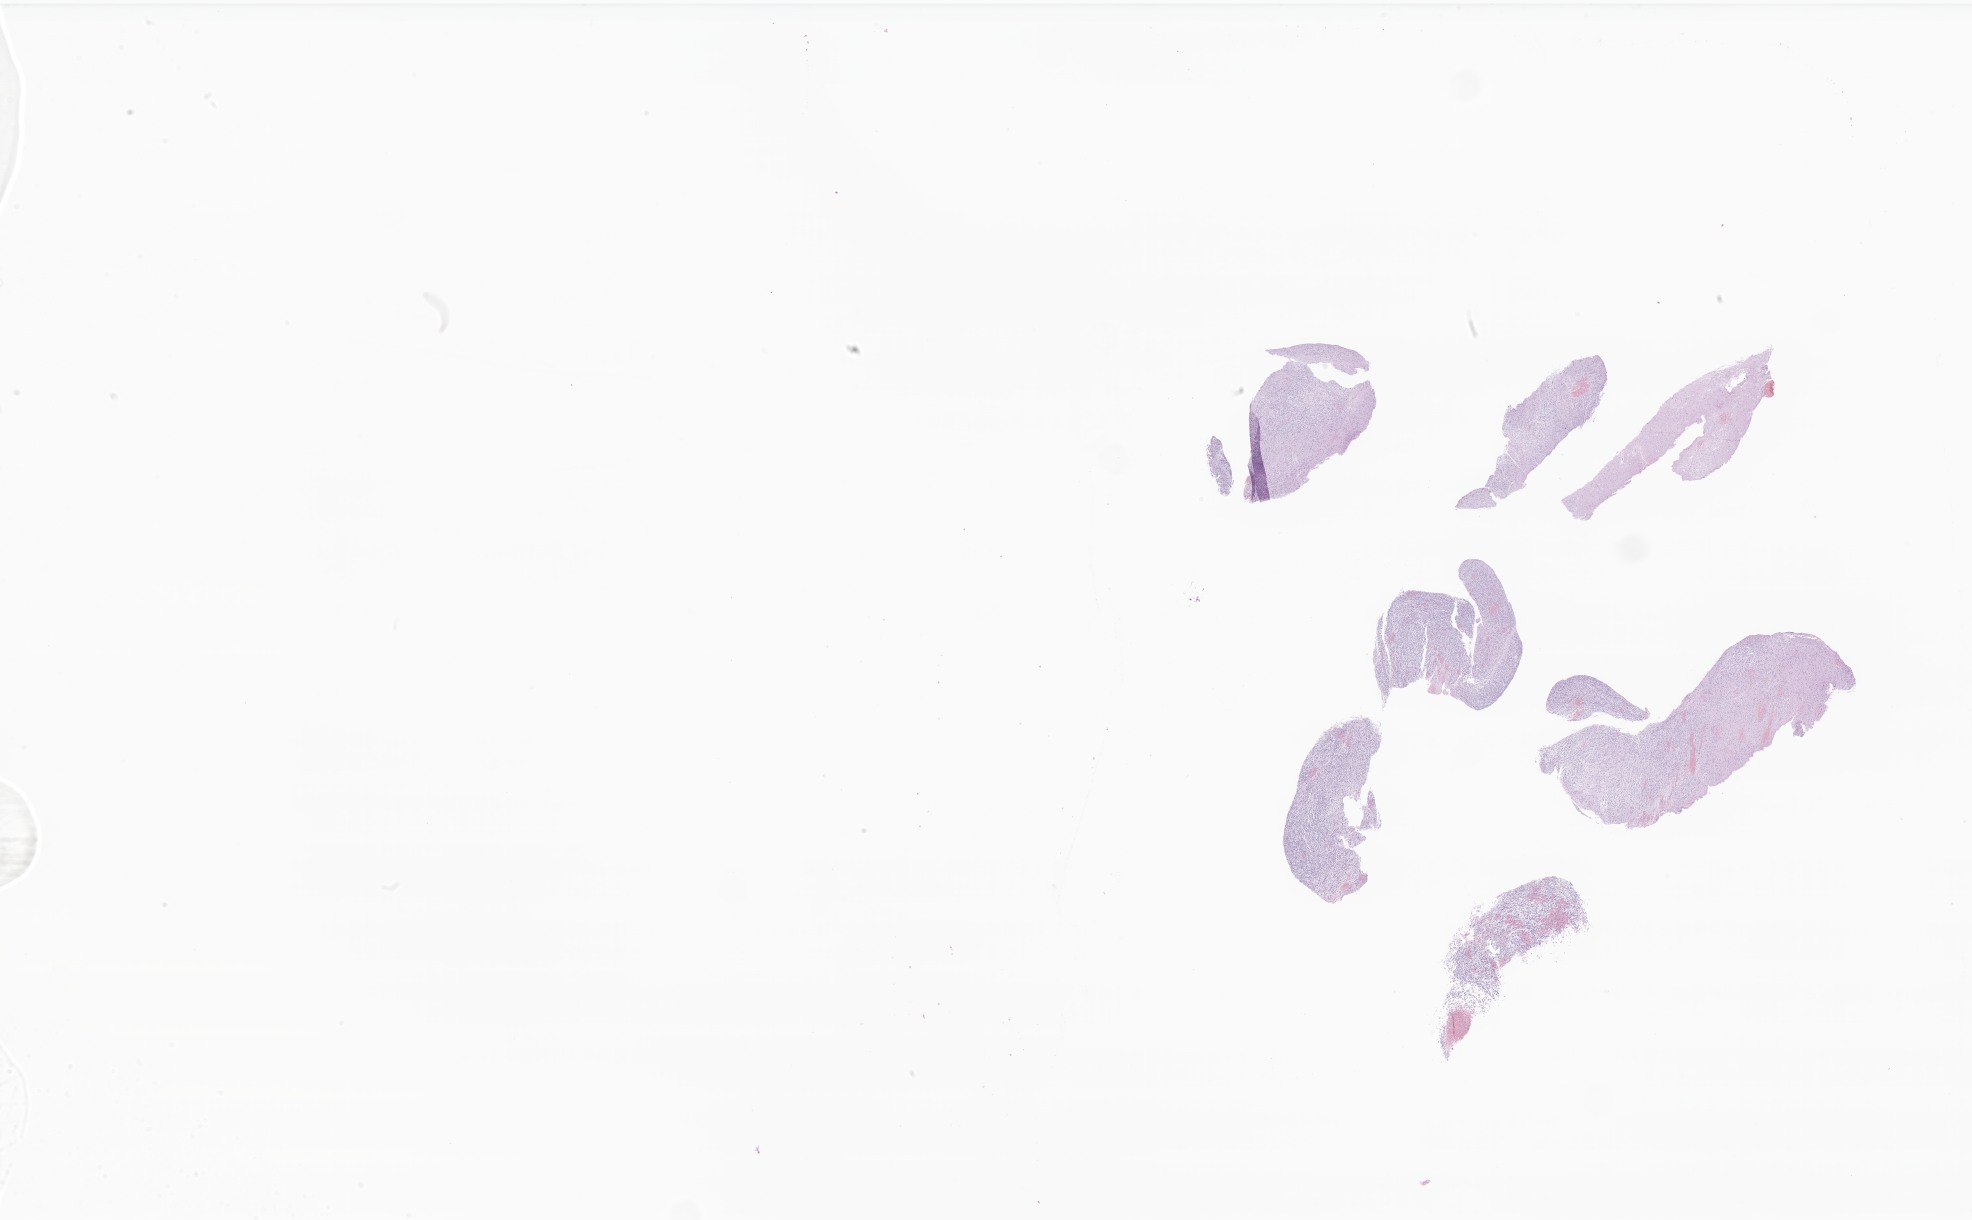
Whole-slide image, H&E stain of tumor tissue from the brain stem — low-resolution overview of the scanned area, about 33.3 x 20.6 mm, formalin-fixed, paraffin-embedded (FFPE) tissue. Female patient, age 126 months (10 years 6 months).
Recorded diagnosis: Glioma, malignant.